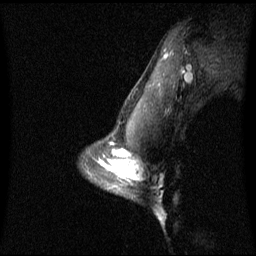
Breast MRI (dynamic contrast-enhanced), one sagittal slice. Slice 49 of 60 in the series (ordered by position). Dynamic contrast-enhanced series, image 2 of 3 at this slice position (ordered by acquisition). 1.5 T. TE 4.2 ms, TR 8.4 ms. 256 × 256 image matrix. Patient: female, 42 years. From the clinical record (not read from this slice): setting: breast cancer imaged before/during neoadjuvant chemotherapy; receptor status: triple-negative.
Structures marked on this image (semi-automatic segmentation, software-assisted and operator-edited):
- analysis volume of interest (the breast-tissue region the enhancement analysis was run in; not a lesion): box from (x=106, y=156) to (x=137, y=191) px
- tumour enhancement mask (voxels above the 70 % enhancement threshold inside the analysis volume of interest): (x=123, y=162)–(x=136, y=179)